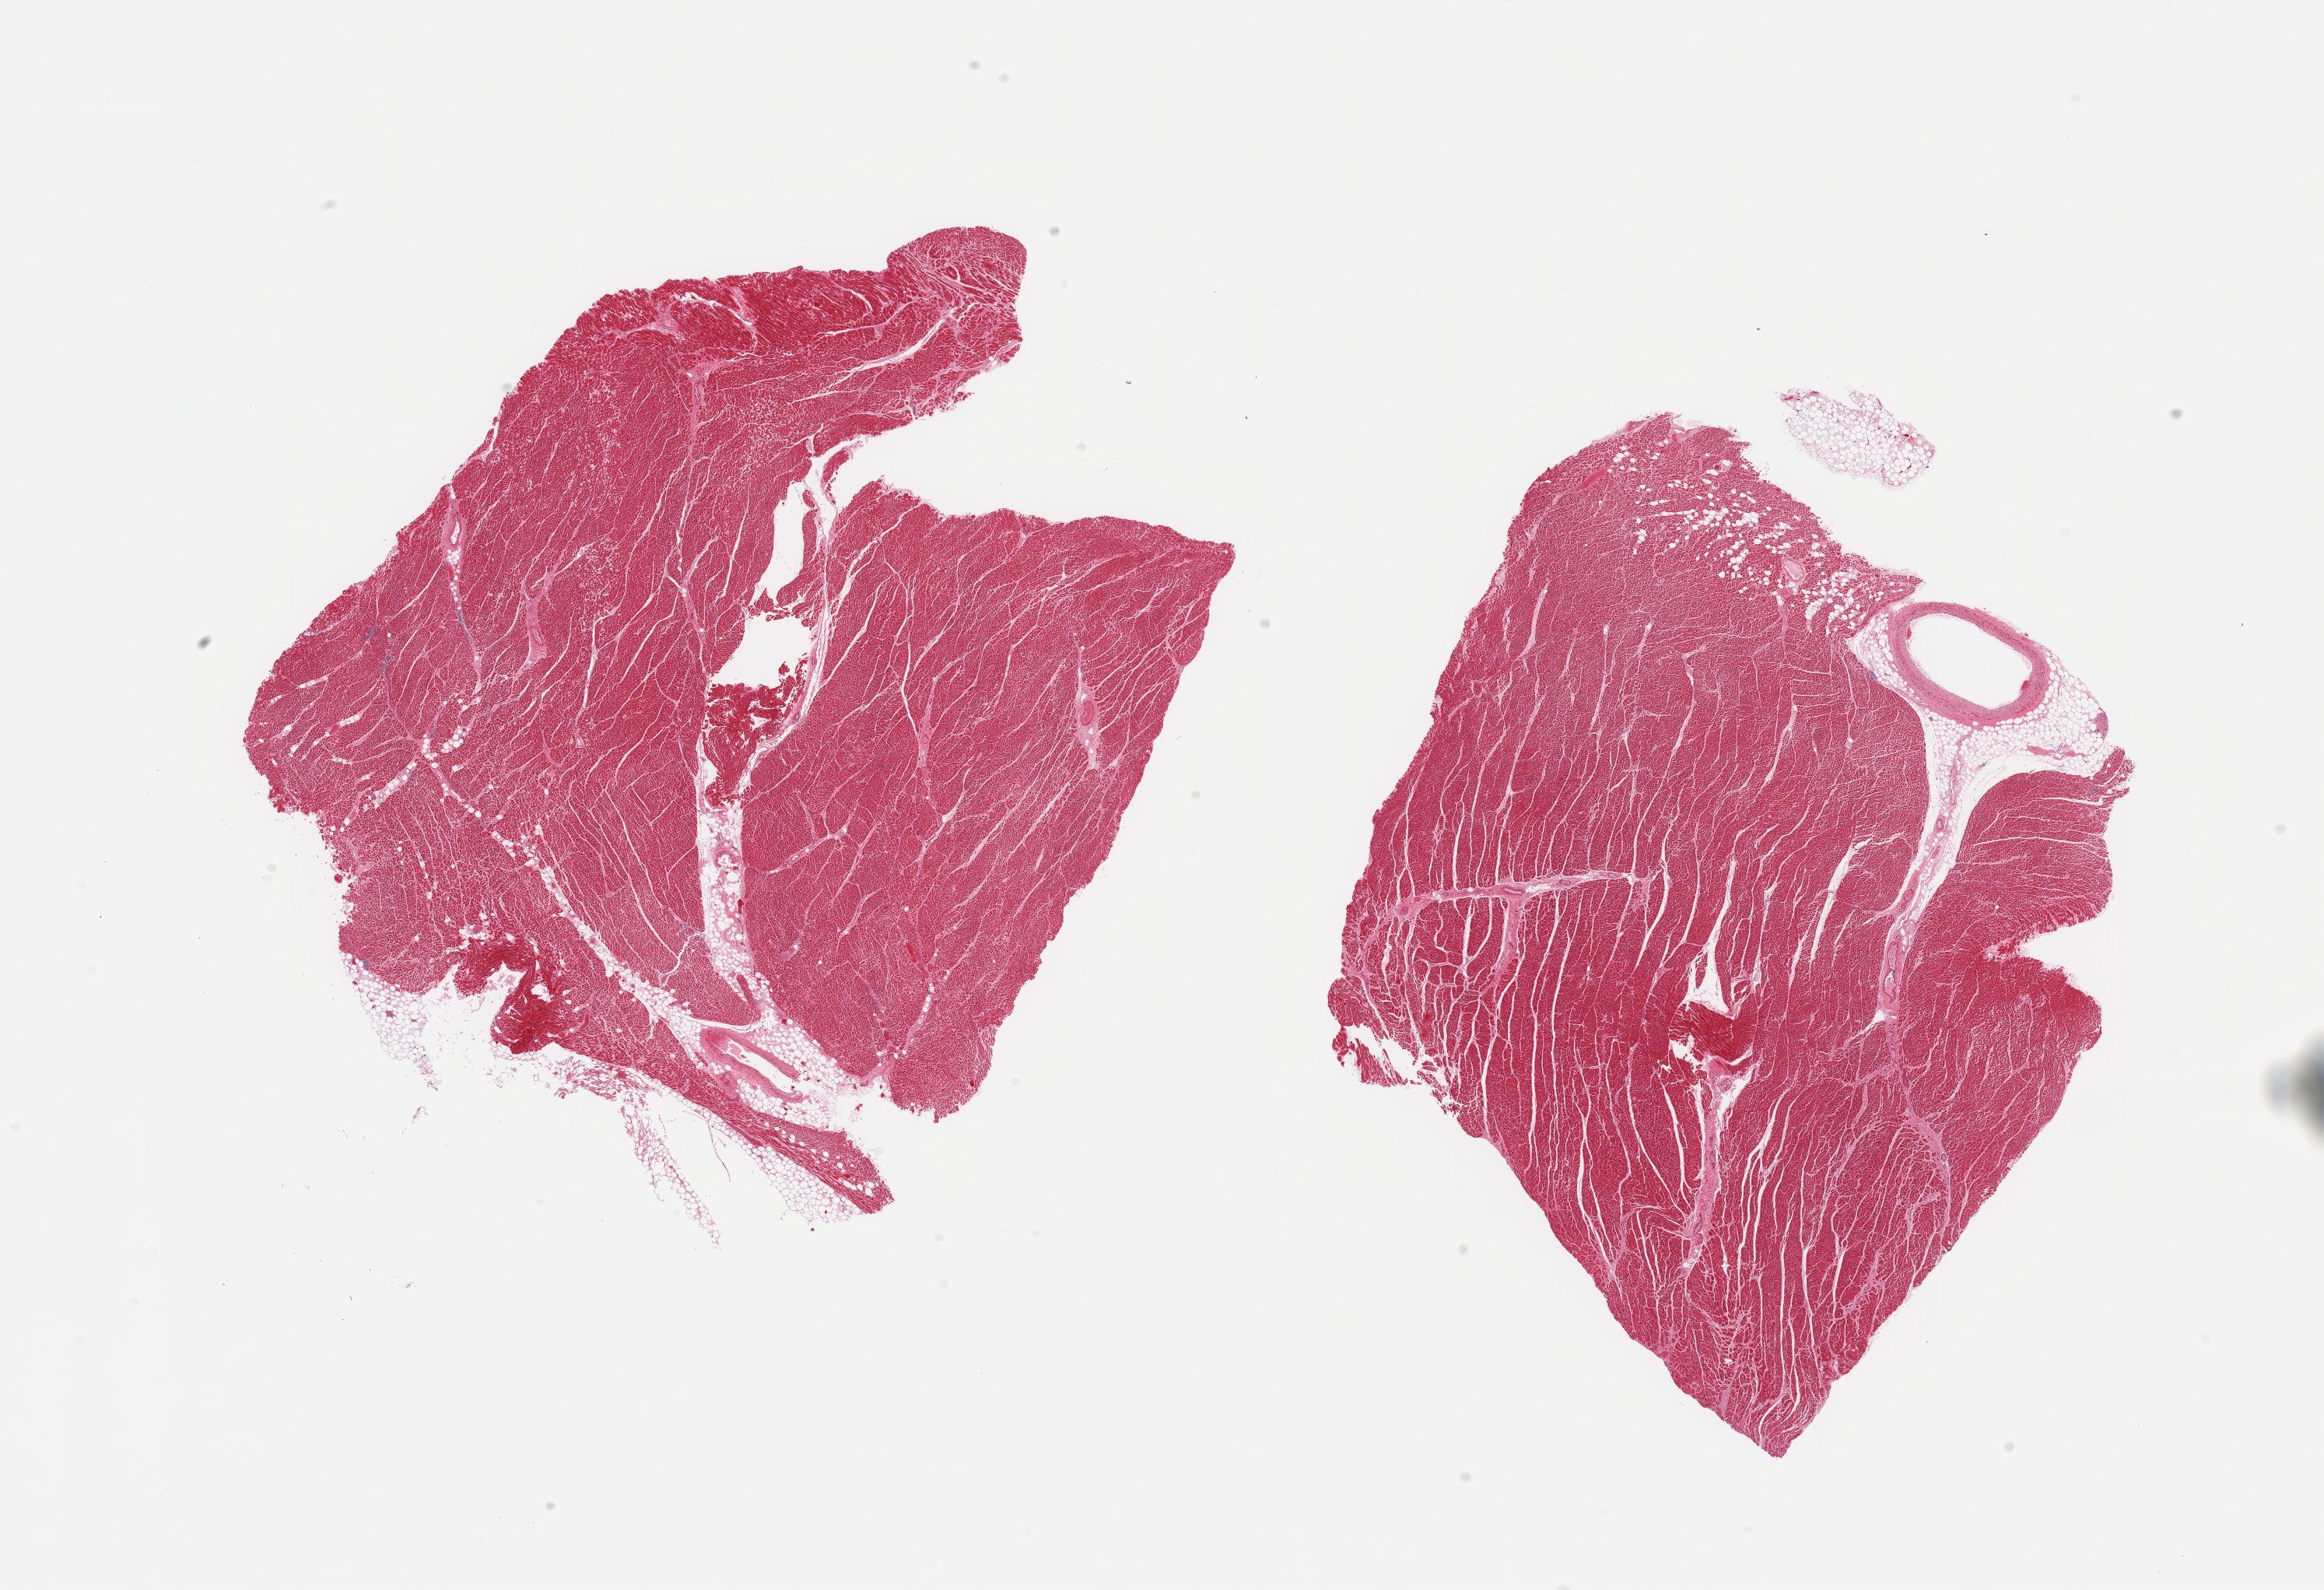
Haematoxylin and eosin whole-slide image, shown as a low-resolution overview of the whole scanned area (about 23.6 x 16.2 mm). PAXgene-fixed, paraffin-embedded tissue. Target tissue: heart. Tissue donor sample. Male donor.
Reviewer comment on this tissue sample: 2 pieces; mild interstitial fibrosis and internal fat; 1.6mm artery in 1 piece.